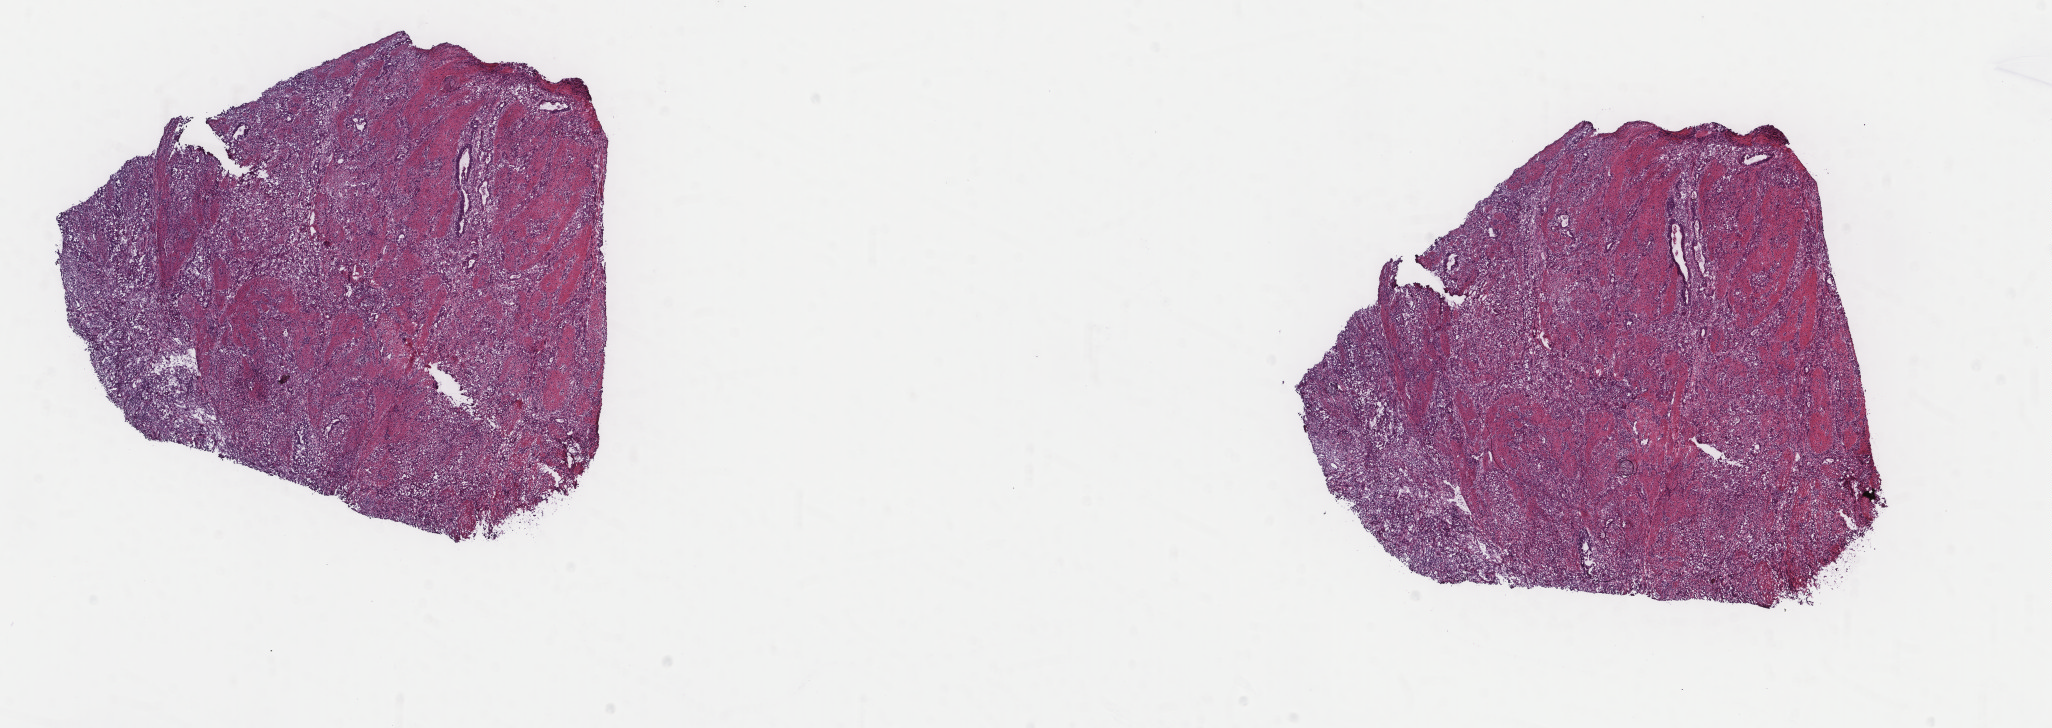
Whole-slide histology image, Hematoxylin and eosin (H&E) stained, whole scanned area (about 16.3 x 5.8 mm, slide scanned at 40x) shown as a low-resolution overview, frozen section, primary tumour sample from the stomach. Male patient; age at initial diagnosis 51 years. Histologic grade: G3 (poorly differentiated). Slide review estimates, as recorded: tumour cells 58%, tumour nuclei 75%, normal cells 0%, stromal cells 40%, necrosis 2%. Infiltration values recorded for this section: lymphocyte infiltration 10%, monocyte infiltration 2%, neutrophil infiltration 2%.
Histologic diagnosis: Adenocarcinoma, intestinal type (fundus of stomach). AJCC pathologic stage: IIIA (7th edition).